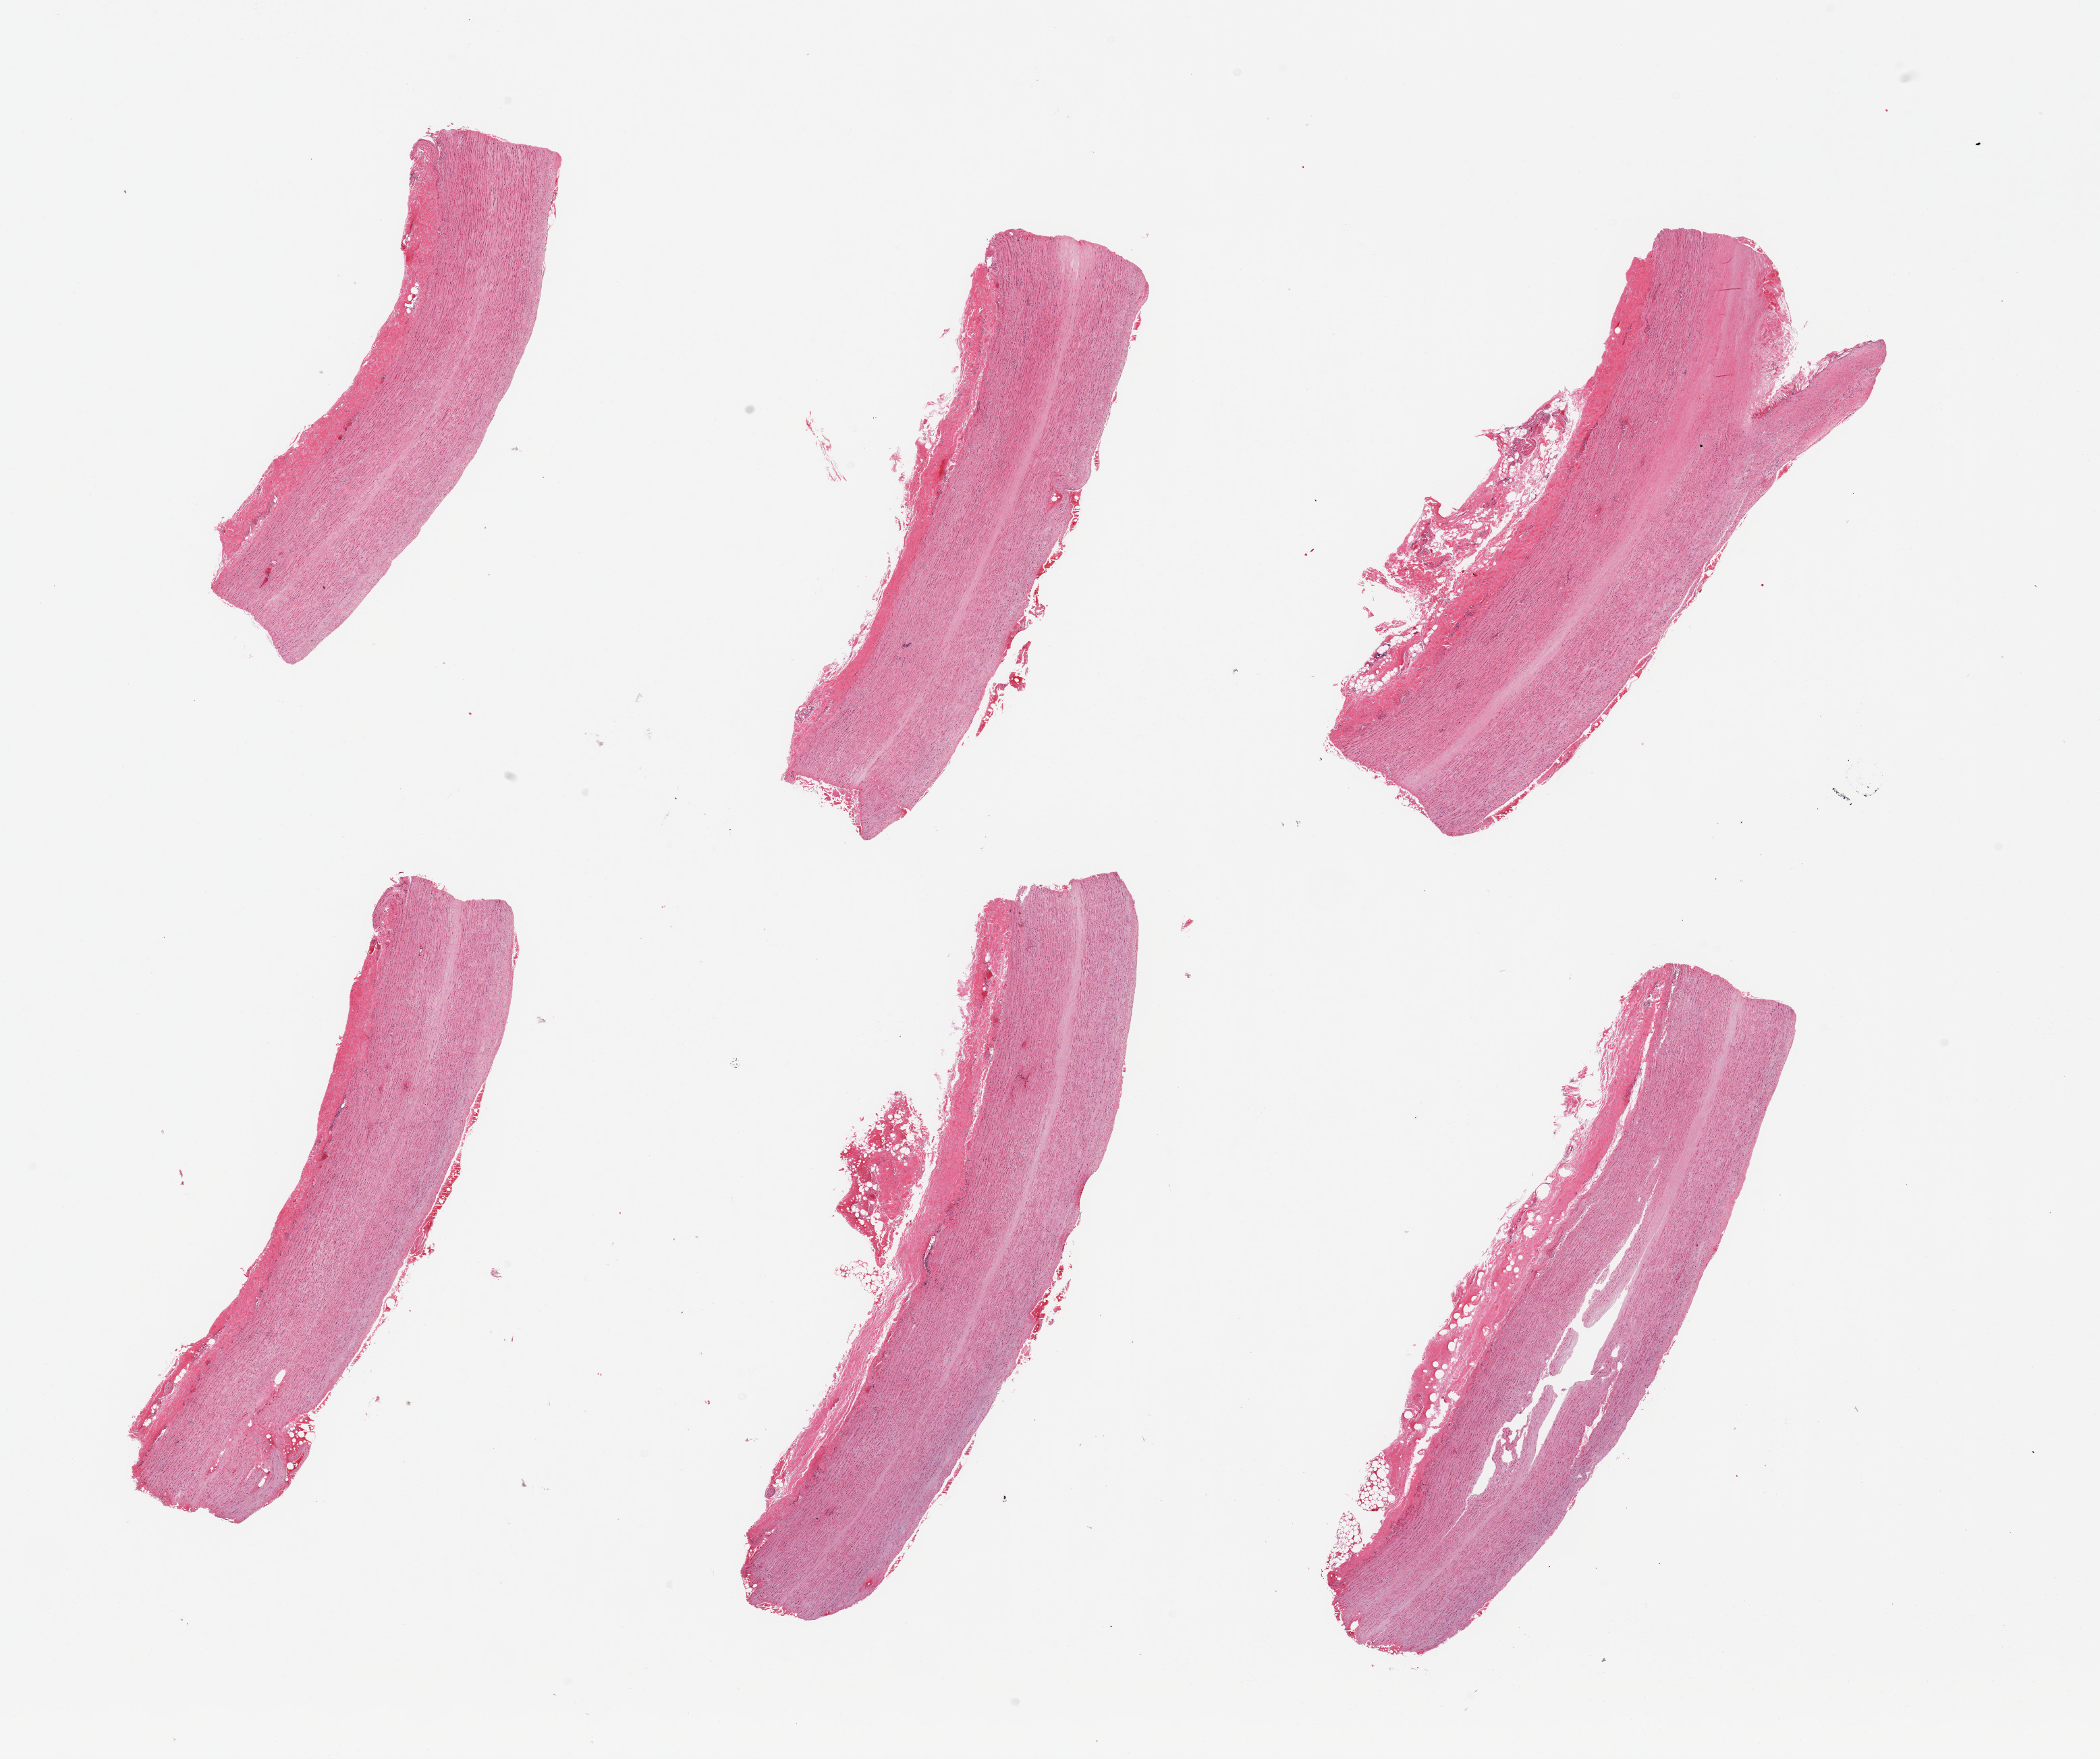
H&E whole-slide image, whole scanned area (about 24.6 x 20.6 mm) shown as a low-resolution overview, PAXgene-fixed paraffin-embedded (PFPE) section, sampled site (target tissue): aorta, tissue donor sample. Donor sex: male.
* pathologist's review note for this sample: 6 pieces, atherosis up to ~1mm